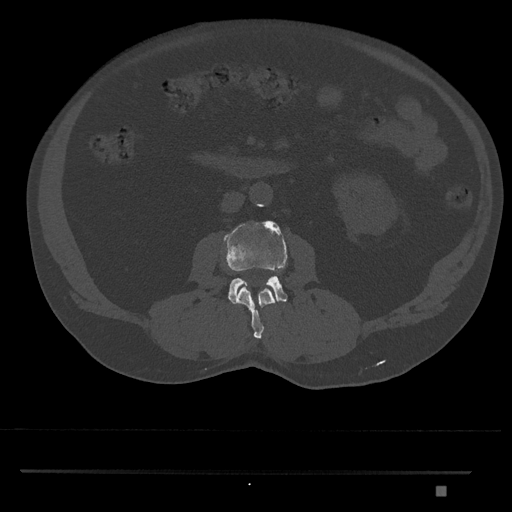
CT including the spine, one axial slice. Slice 714 of 1134 in the series (ordered by position). 120 kVp. Bone window (W 1800 / L 400 HU). 0.5 mm slice thickness. 512 × 512 image matrix, field of view 429 × 429 mm. Male patient, age 65 years. From the clinical record (not read from this slice): primary cancer: prostate.
Structures marked on this image (semi-automatically segmented with operator editing):
- L2 vertebra: bounding box (x1, y1, x2, y2) in pixels: (237, 286, 275, 339)
- L3 vertebra: (223, 220, 287, 305)